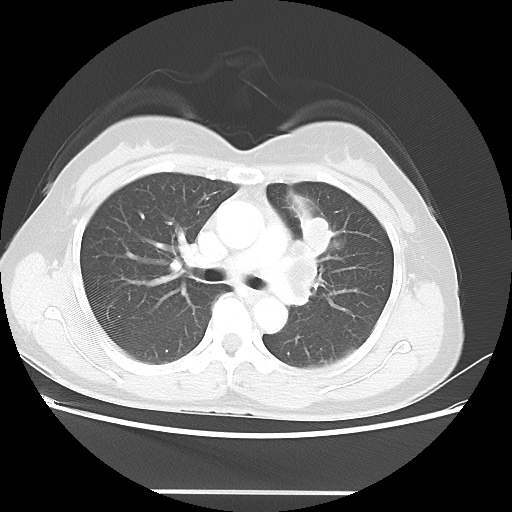
Chest CT, one axial slice. Slice 28 of 46 in the series (ordered by position). Reconstruction kernel LUNG. Lung window (W 1500 / L -600 HU). 5 mm slice thickness. 512 × 512 image matrix, field of view 360 × 360 mm. Patient: female, 50 years. Case-level facts recorded for this patient, not image findings: clinical TNM (as recorded): T1c N1 M0; histopathological grade: G3.
Structures marked on this image (rectangle marked by the reading radiologist):
- lung tumour (recorded histology: adenocarcinoma): bounding box <294,210,333,255> (left, top, right, bottom; pixels)